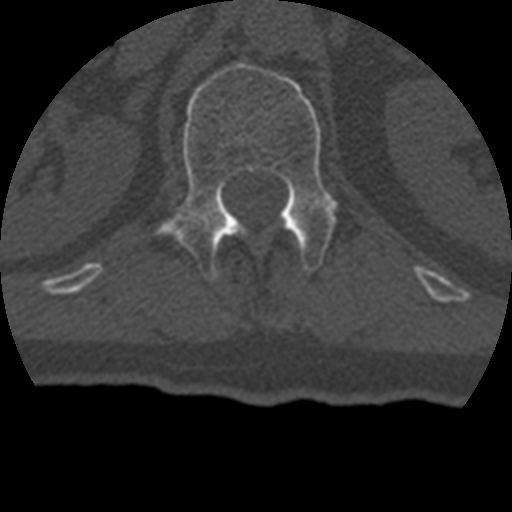
CT including the spine, one axial slice; position 151 of 399 along the scan axis; 120 kVp; bone window (W 1800 / L 400 HU); 1.25 mm slice thickness; 512 × 512 image matrix, field of view 160 × 160 mm. Patient age 69 years. Case-level facts recorded for this patient, not image findings: primary cancer: prostate.
Outlined on this slice (semi-automatic segmentation, software-assisted and operator-edited):
- L1 vertebra: bounding box <156,62,339,280> (left, top, right, bottom; pixels)